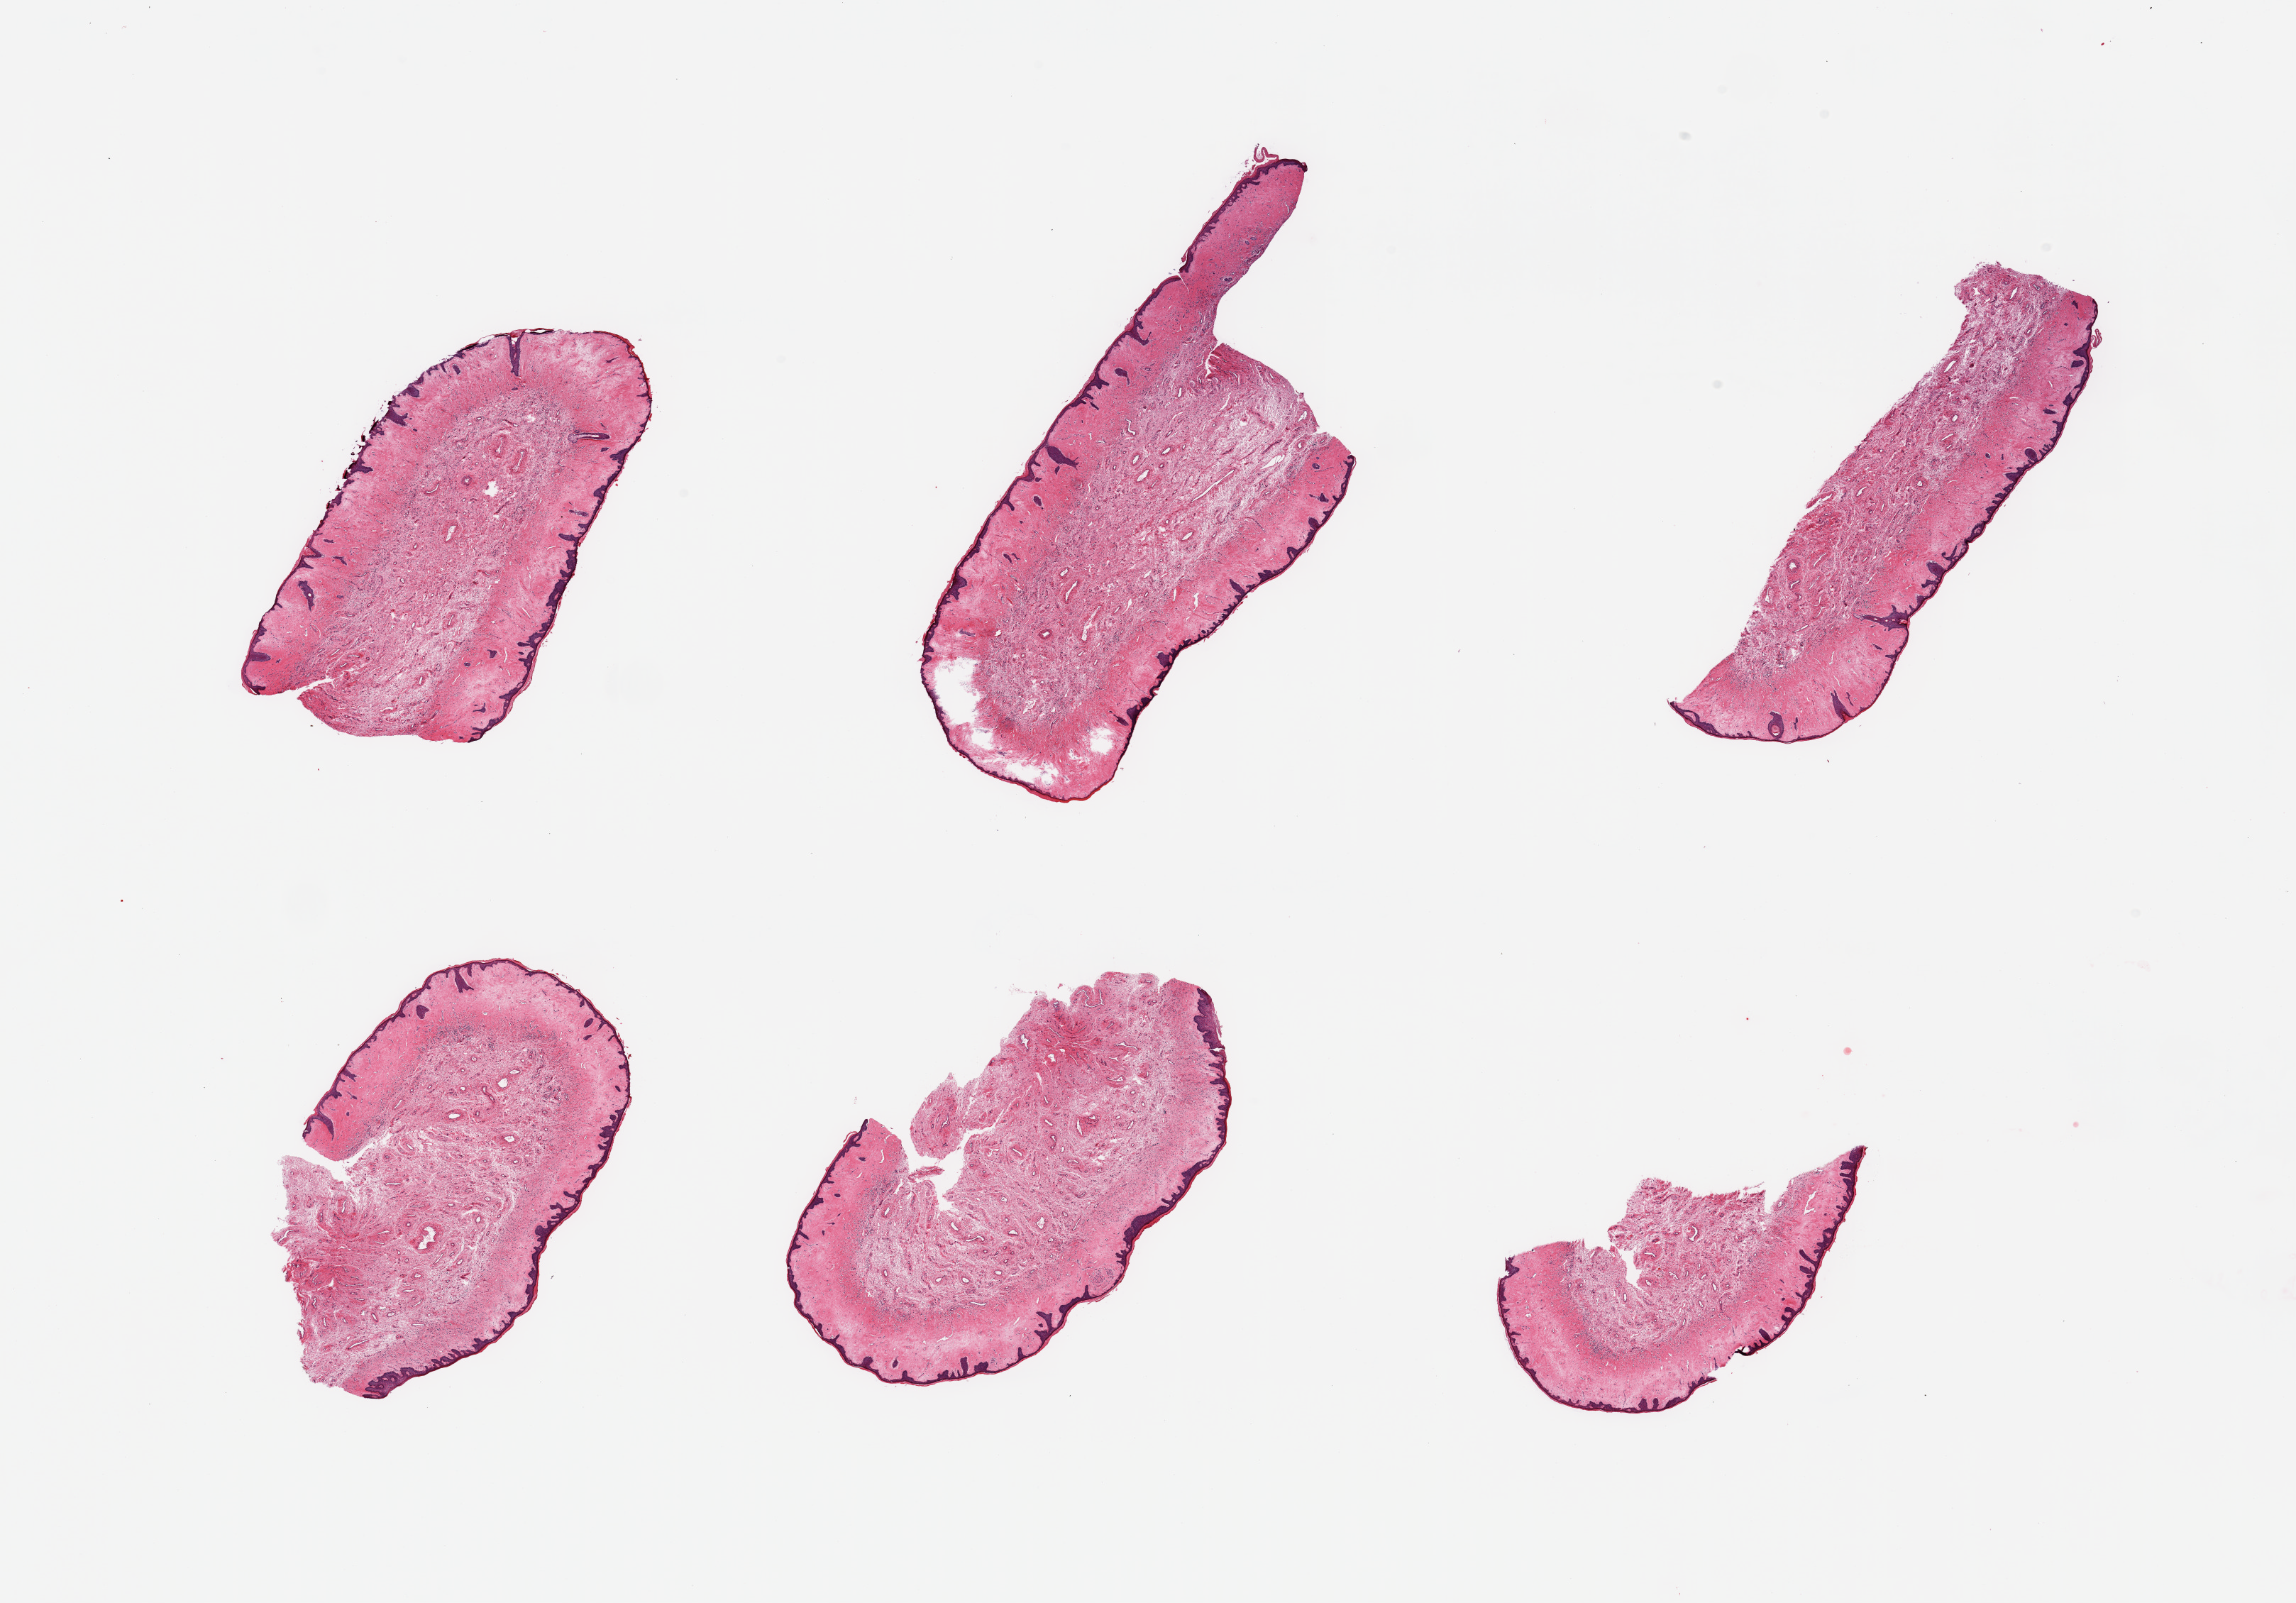
Digitized H&E-stained section, brightfield — shown as a low-resolution overview of the whole scanned area (about 25.6 x 17.9 mm), PAXgene-fixed paraffin-embedded (PFPE) section, target tissue: vagina, tissue donor sample. Donor: female.
Review note (as recorded): 6 pieces; sample is keratinized and has skin appendages: labia not target vagina.